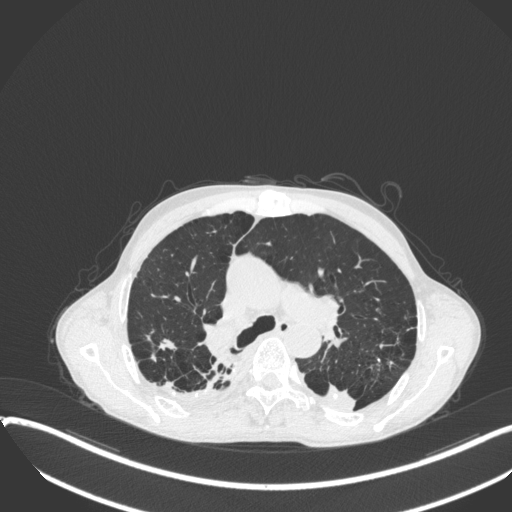
Chest CT, one axial slice. Position 258 of 400 along the scan axis. 120 kVp. Lung window (W 1500 / L -600 HU). 1 mm slice thickness. 512 × 512 image matrix, field of view 400 × 400 mm. Male patient, age 57 years. From the clinical record (not read from this slice): clinical TNM (as recorded): T4 N0 M0.
Outlined on this slice (rectangle marked by the reading radiologist):
- lung tumour (recorded histology: squamous cell carcinoma): box from (x=310, y=380) to (x=362, y=414) px